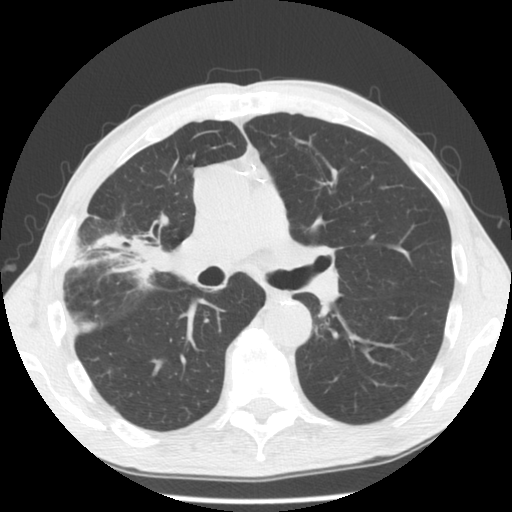
Chest CT (low-dose screening protocol), one axial image. Third annual screen. Lung window (W 1500 / L -600 HU). Slice 77 of 132 in the series. Male participant, aged 57 years at enrolment. Former smoker at enrolment.
• Expert-annotated lung lesion, bounding box <60,216,163,316> (left, top, right, bottom; pixels).
• Reader record for this screening exam (exam-level; its link to the box is not recorded): non-calcified nodule or mass ≥4 mm, right upper lobe, 38 × 34 mm, poorly defined margins, mixed attenuation, pre-existing on the prior screen: no.
• Participant outcome: lung cancer diagnosed 76 days after this screen — squamous cell carcinoma, NOS, right upper lobe, stage IA (AJCC 6th edition), 15 mm at pathology.